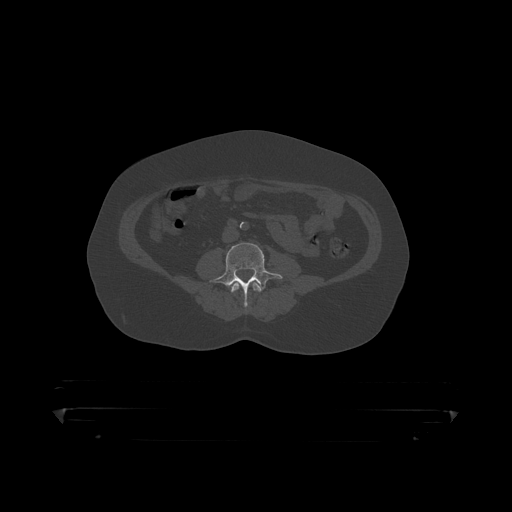
CT including the spine, one axial slice. Slice 69 of 390 in the series (ordered by position). Reconstruction kernel STANDARD. Bone window (W 1800 / L 400 HU). 512 × 512 image matrix. Patient: male, 60 years. Case-level facts recorded for this patient, not image findings: primary cancer: prostate.
Outlined on this slice (semi-automatic segmentation, software-assisted and operator-edited):
- L3 vertebra: bounding box [x1, y1, x2, y2] px = [231, 282, 263, 308]
- L4 vertebra: [209, 243, 283, 306]